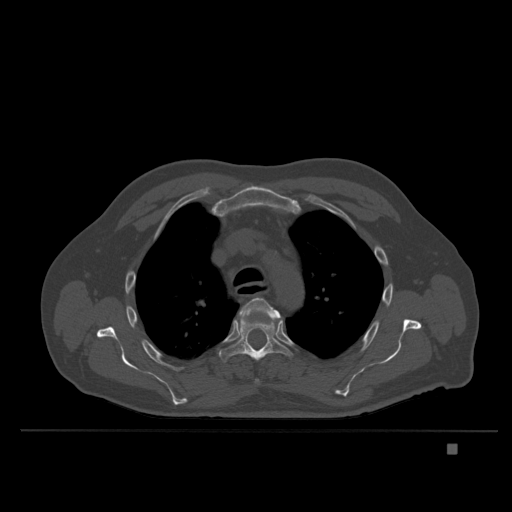
CT including the spine, one axial slice. Position 278 of 435 along the scan axis. Bone window (W 1800 / L 400 HU). 1.5 mm slice thickness. 512 × 512 image matrix. Patient: male, 73 years. Case-level facts recorded for this patient, not image findings: primary cancer: skin.
Outlined on this slice (semi-automatically segmented with operator editing):
- T4 vertebra: box from (x=237, y=297) to (x=281, y=384) px
- T5 vertebra: (x=219, y=318)–(x=294, y=363)